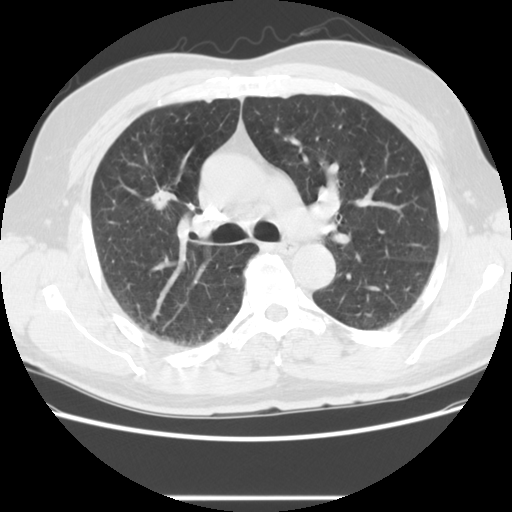
Chest CT (low-dose screening protocol), one axial image, second screening round (one year after baseline), lung window (W 1500 / L -600 HU), 2.5 mm slice thickness, 512 × 512 image matrix, field of view 360 × 360 mm. Male participant, aged 59 years at enrolment. Current smoker at enrolment.
Expert reader's lesion annotation, bounding box <139,180,179,219> (left, top, right, bottom; pixels). Screening reader's record for this exam (one nodule recorded; not confirmed to be the boxed lesion): non-calcified nodule or mass ≥4 mm, right upper lobe, 20 × 13 mm, spiculated (stellate) margins, soft tissue attenuation, pre-existing on the prior screen: yes; interval growth: yes. Participant outcome: lung cancer diagnosed 267 days after this screen — large cell carcinoma, NOS, right upper lobe, poorly differentiated (G3), stage IIIA (AJCC 6th edition), 34 mm at pathology.